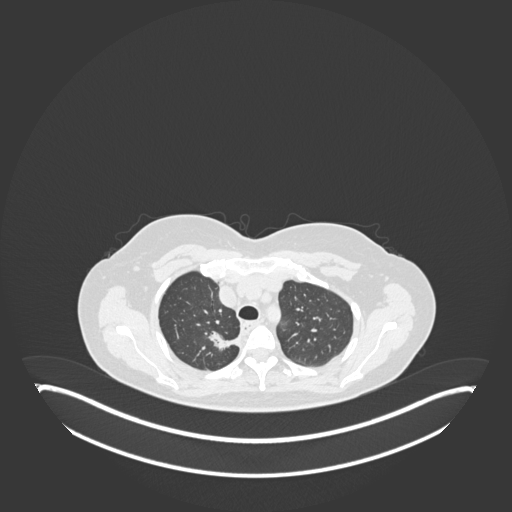
Chest CT, one axial slice; position 140 of 181 along the scan axis; 120 kVp; lung window (W 1500 / L -600 HU); 1 mm slice thickness; 512 × 512 image matrix, field of view 500 × 500 mm. Patient: female, 65 years. Case-level facts recorded for this patient, not image findings: clinical TNM (as recorded): T1b N0 M0; histopathological grade: G2.
Annotated regions visible in this slice (bounding box drawn by a radiologist):
- lung tumour (recorded histology: adenocarcinoma): bounding box (x1, y1, x2, y2) in pixels: (205, 327, 241, 350)